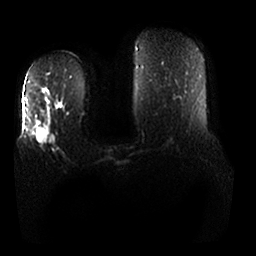
Breast MRI, one axial slice; slice 11 of 25 in the series (ordered by position); diffusion-weighted series; image 2 of 4 stored at this slice position (different b-values; order by instance number); 1.5 T; 256 × 256 image matrix. Female patient.
Structures marked on this image (outlined manually by an expert reader):
- tumour on diffusion-weighted imaging: bounding box <37,135,49,147> (left, top, right, bottom; pixels)